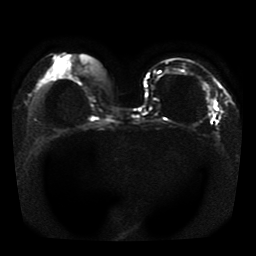
Breast MRI, one axial slice; position 13 of 41 along the scan axis; diffusion-weighted series; image 2 of 4 stored at this slice position (different b-values; order by instance number); 1.5 T; 5 mm slice thickness; 256 × 256 image matrix, field of view 330 × 330 mm. Female patient.
Annotated regions visible in this slice (expert manual segmentation):
- tumour on diffusion-weighted imaging: bounding box (x1, y1, x2, y2) in pixels: (208, 105, 214, 109)